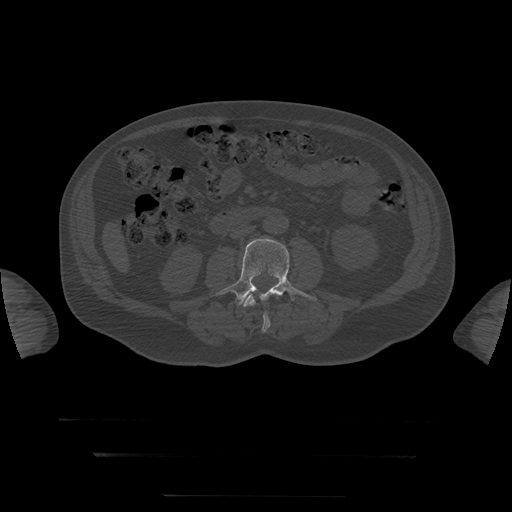
CT including the spine, one axial slice; position 1 of 397 along the scan axis; 120 kVp; bone window (W 1800 / L 400 HU); 512 × 512 image matrix. Patient age 73 years. From the clinical record (not read from this slice): primary cancer: prostate.
Structures marked on this image (semi-automatic segmentation, software-assisted and operator-edited):
- L3 vertebra: box from (x=218, y=238) to (x=318, y=306) px